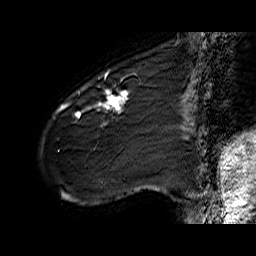
Breast MRI (dynamic contrast-enhanced), one sagittal slice. Slice 15 of 60 in the series (ordered by position). Dynamic contrast-enhanced series, time point 2 of 6 at this slice position (early post-contrast). 1.5 T. TE 6.4 ms, TR 32.9 ms. 4 mm slice thickness. 256 × 256 image matrix, field of view 200 × 200 mm. Female patient. From the clinical record (not read from this slice): setting: breast cancer imaged before/during neoadjuvant chemotherapy; receptor status: HER2-positive.
Outlined on this slice (semi-automatic segmentation, software-assisted and operator-edited):
- analysis volume of interest (the breast-tissue region the enhancement analysis was run in; not a lesion): bounding box <61,77,141,142> (left, top, right, bottom; pixels)
- tumour enhancement mask (voxels above the 100 % enhancement threshold inside the analysis volume of interest): <61,77,129,126>